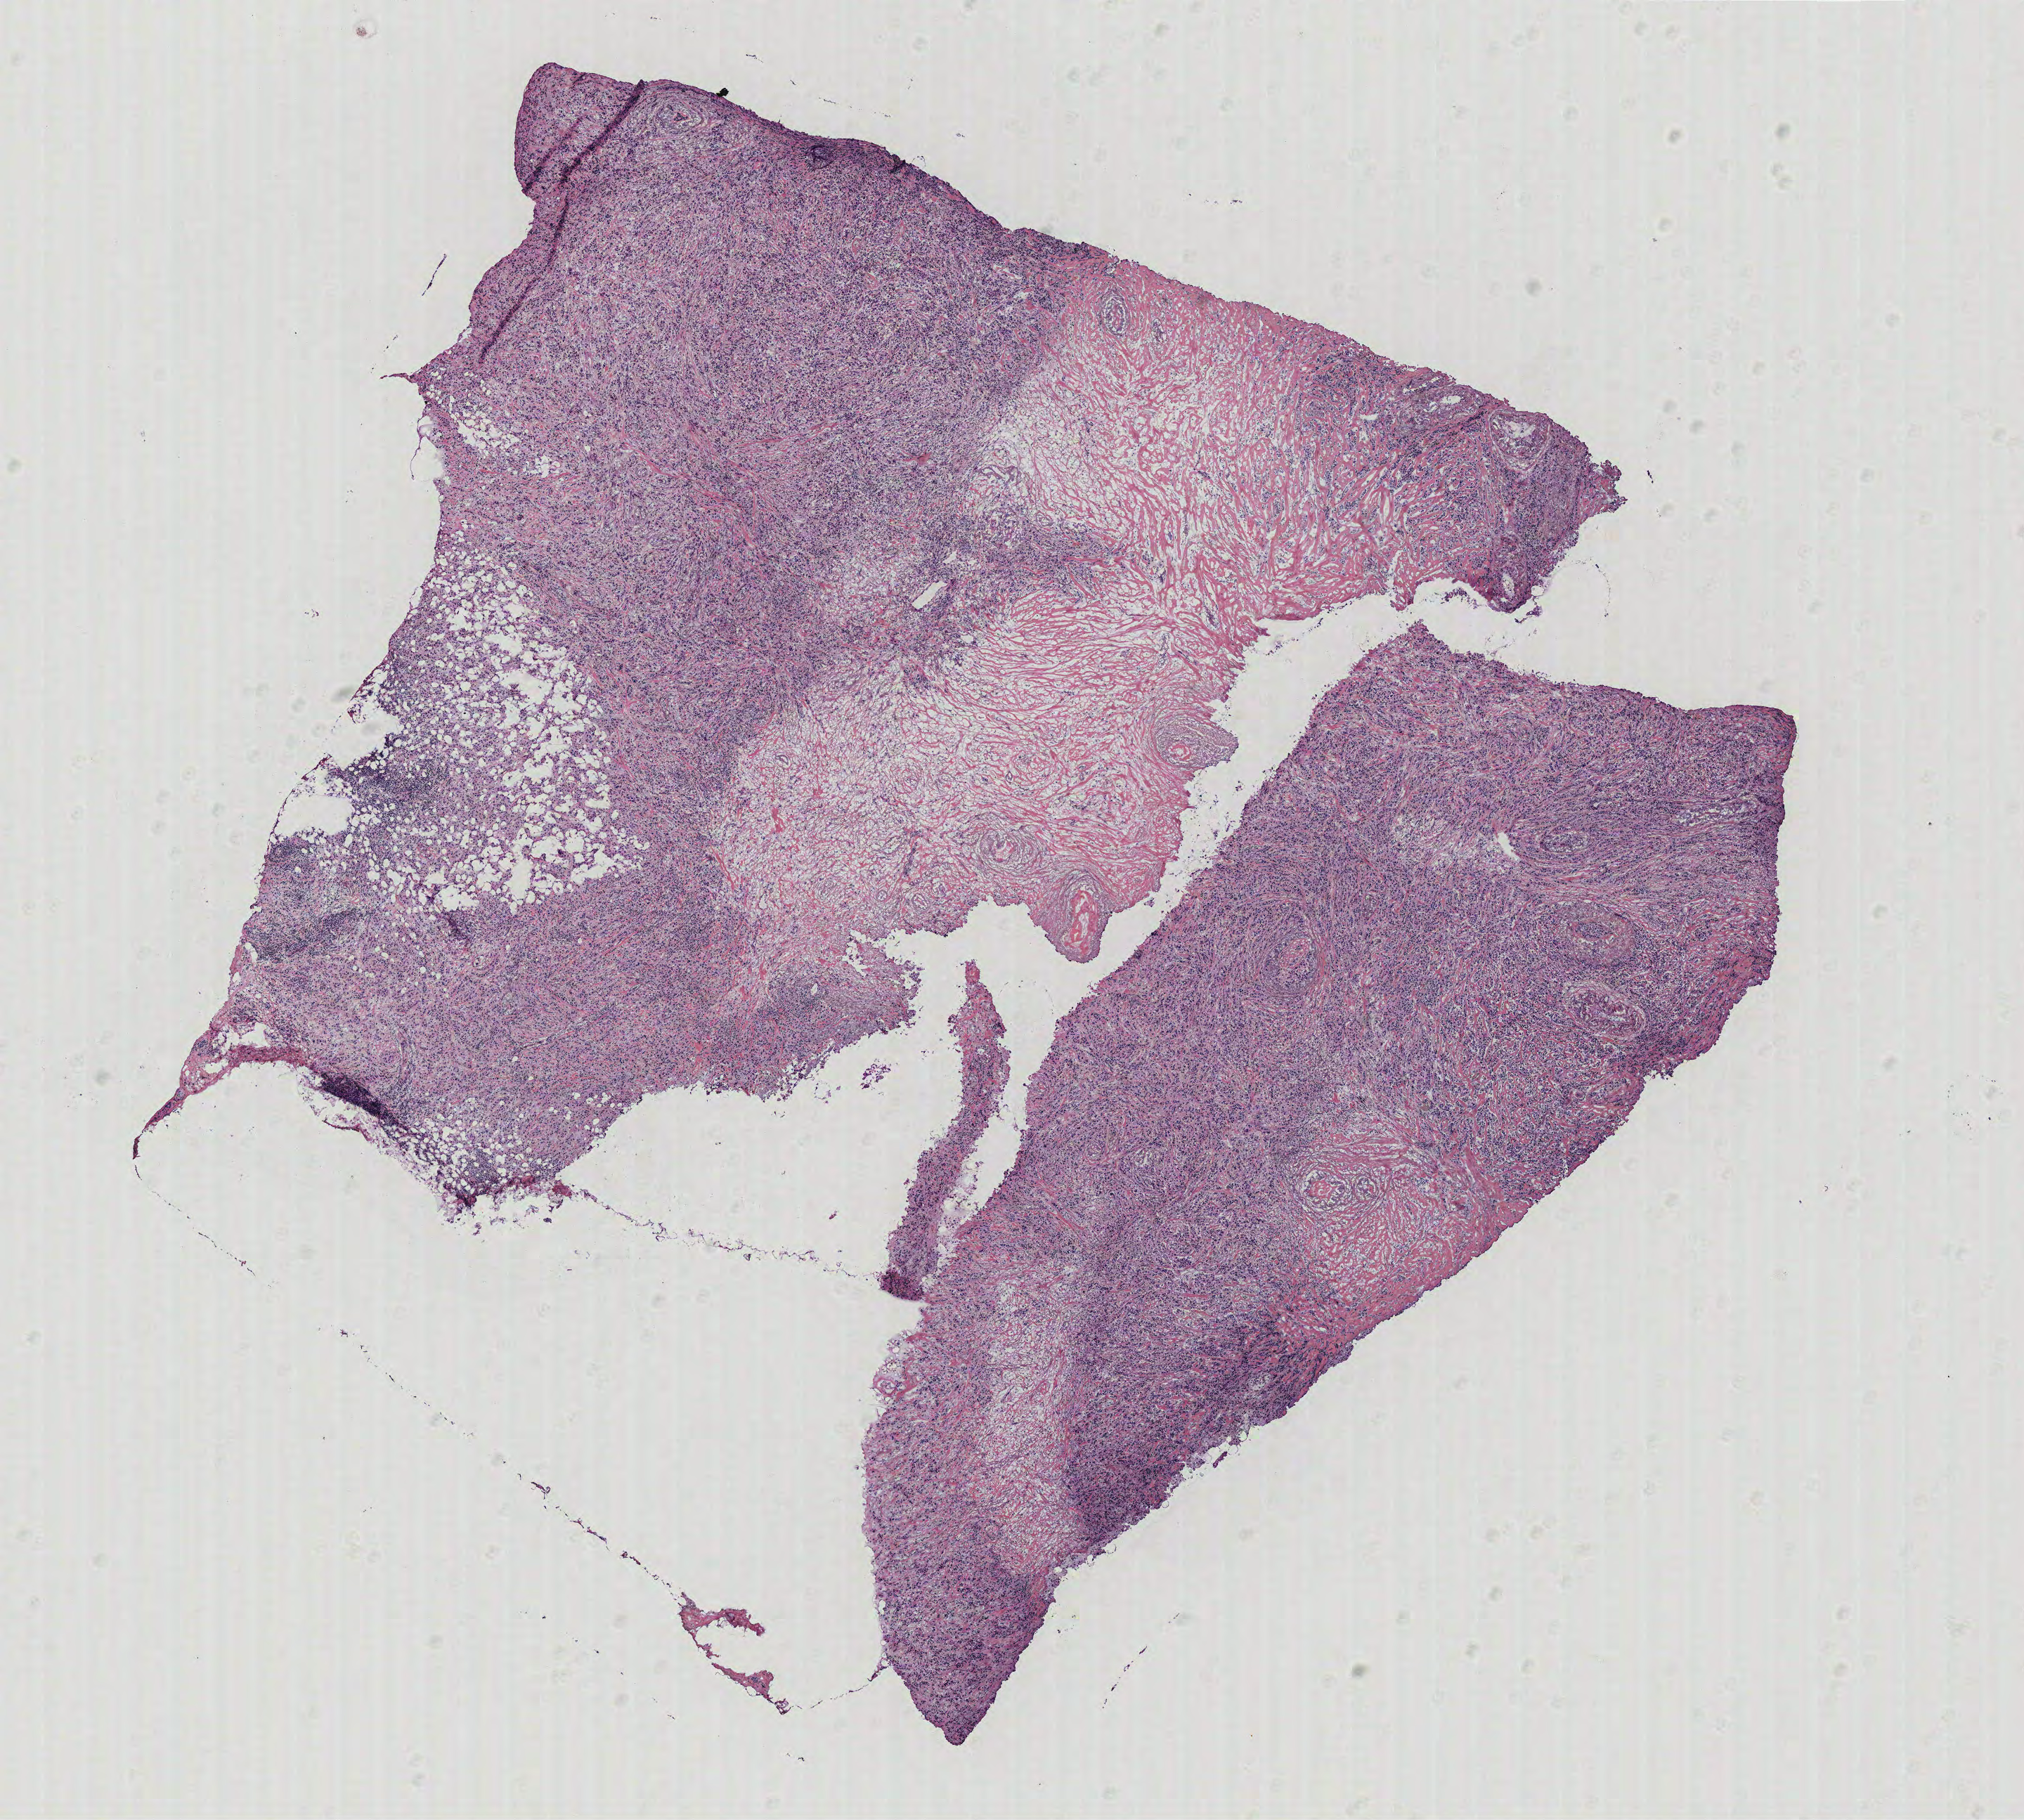
Whole-slide histology image, H&E-stained, low-resolution overview of the scanned area, about 11.5 x 10.4 mm. Breast, tissue type not recorded.
Patient diagnosis (cohort enrolment): breast cancer (breast).